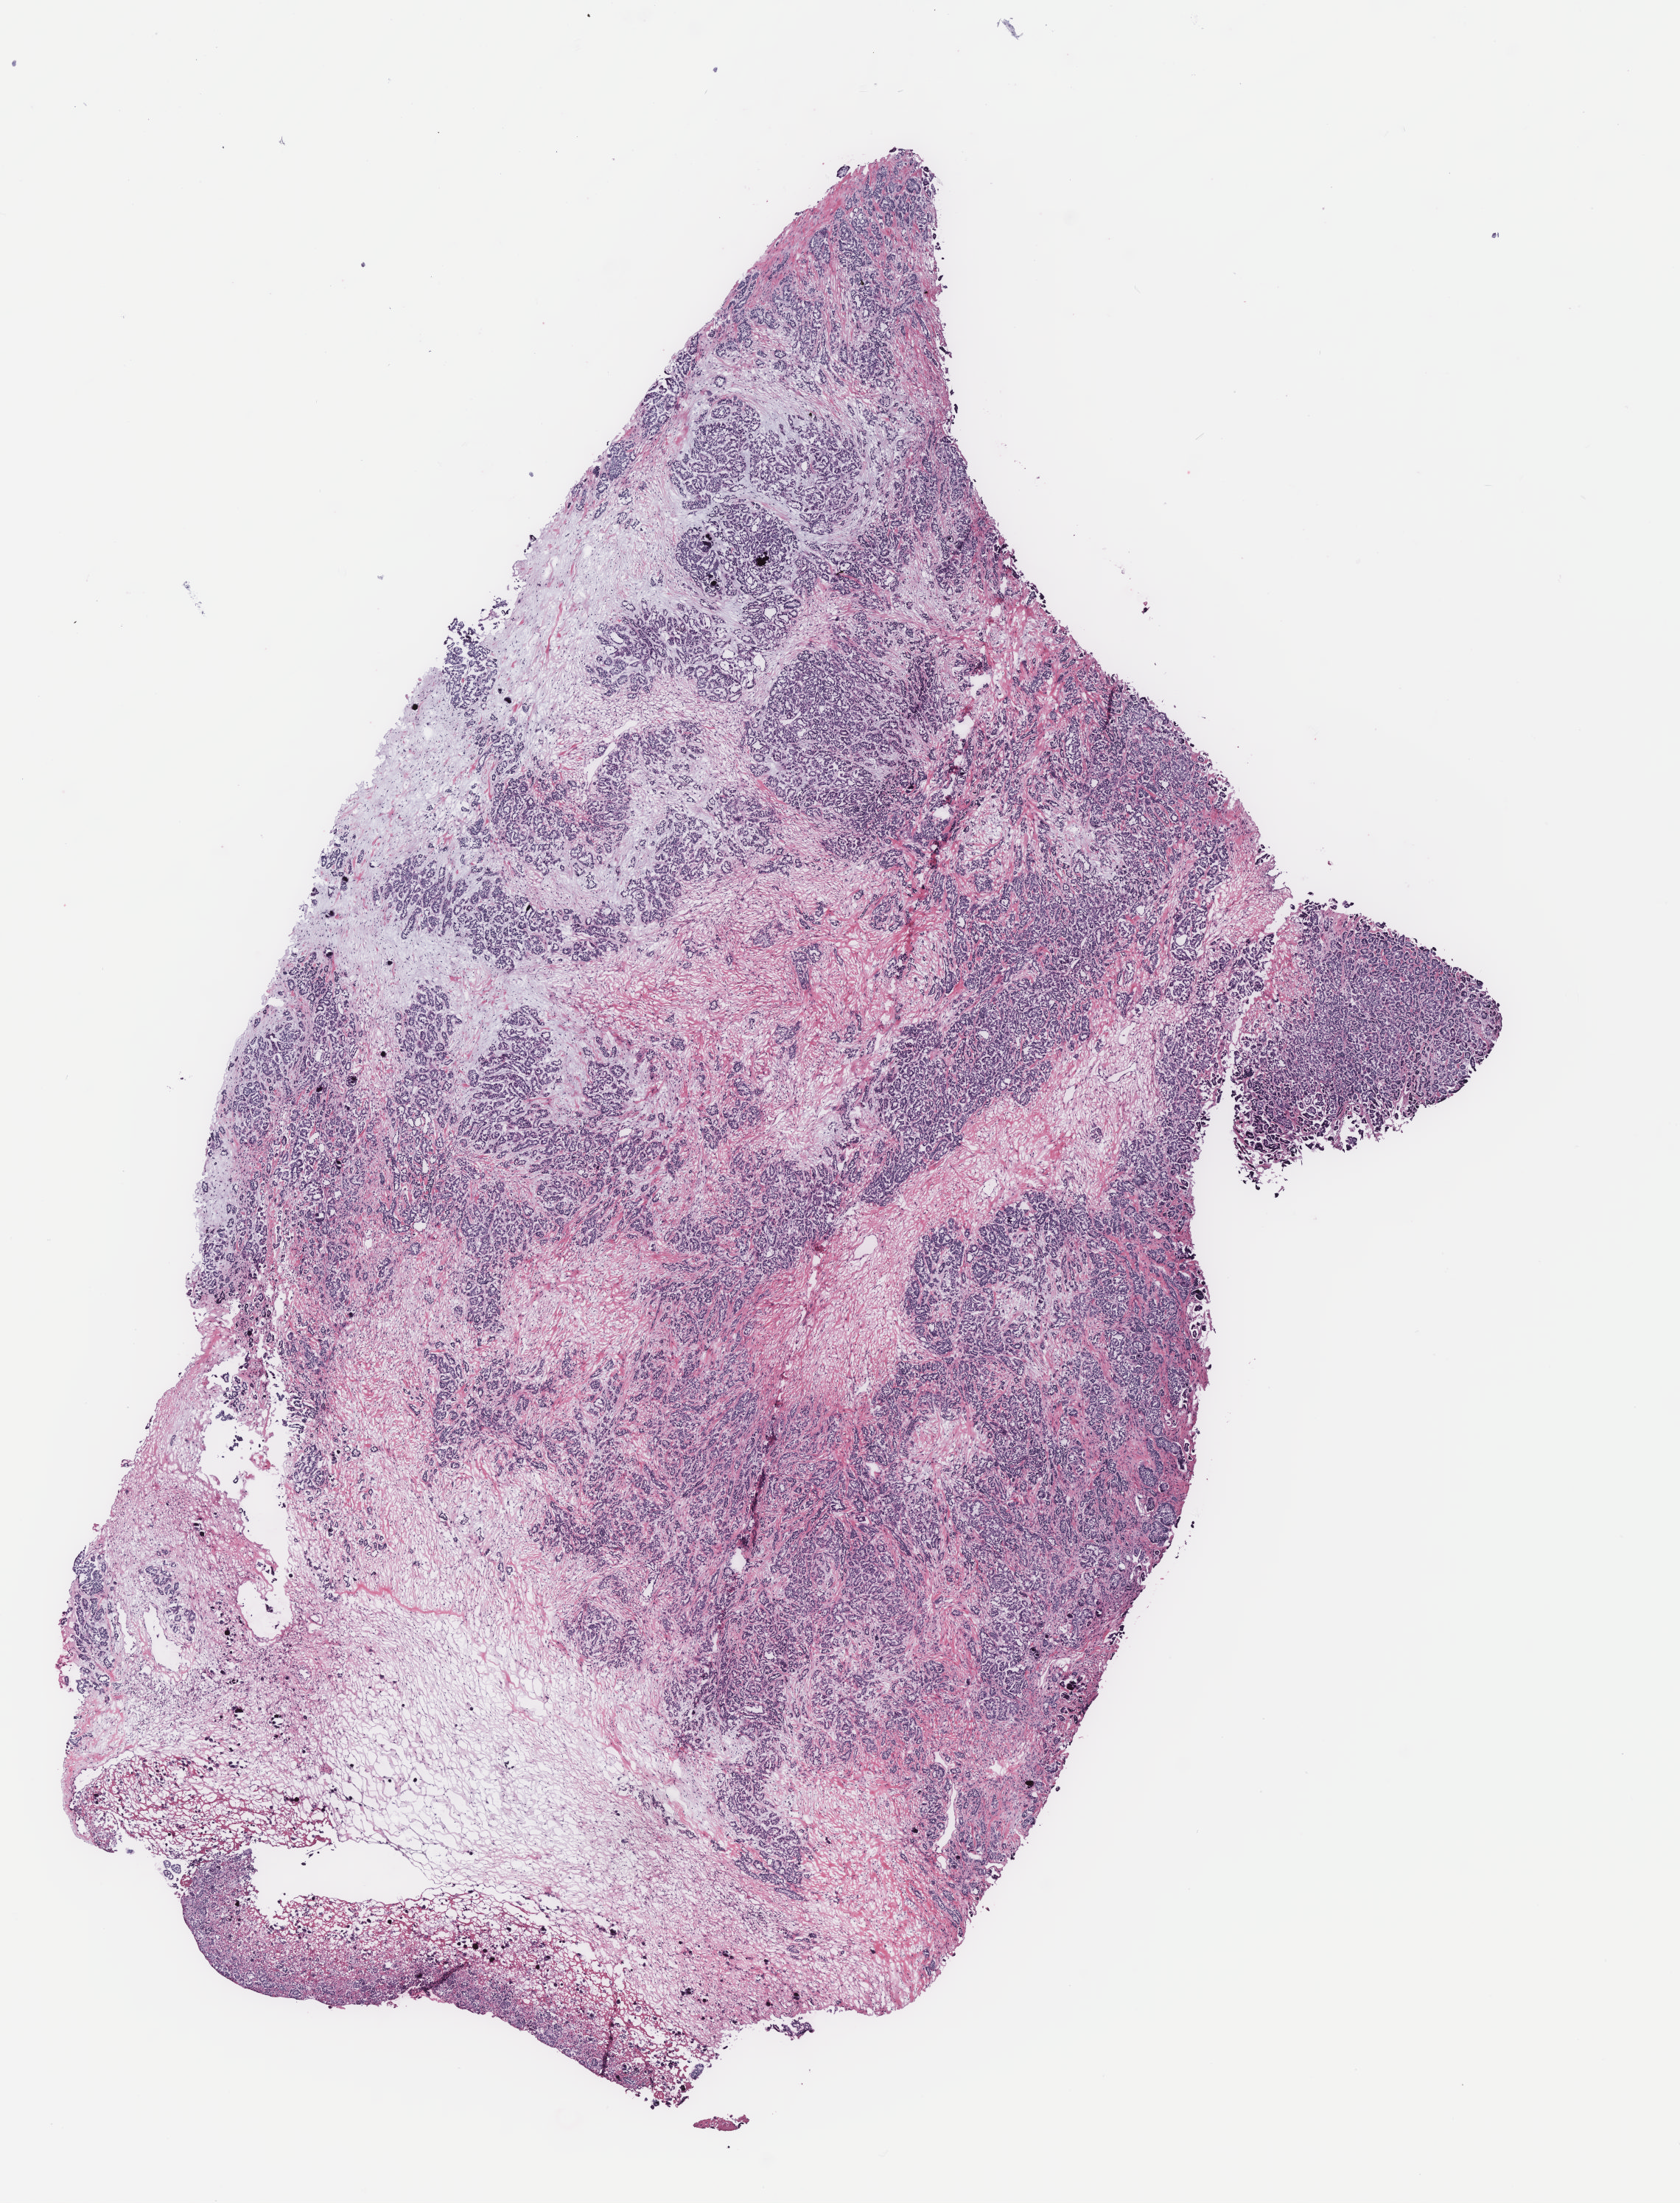
Digitized Hematoxylin and eosin (H&E) stained tissue section (whole slide), whole scanned area (about 9.1 x 12.0 mm) shown as a low-resolution overview; tumour tissue sample, ovary. Patient: female, age 57 years.
• histologic diagnosis: Serous adenocarcinoma, NOS
• primary tumour site (as recorded): ovary